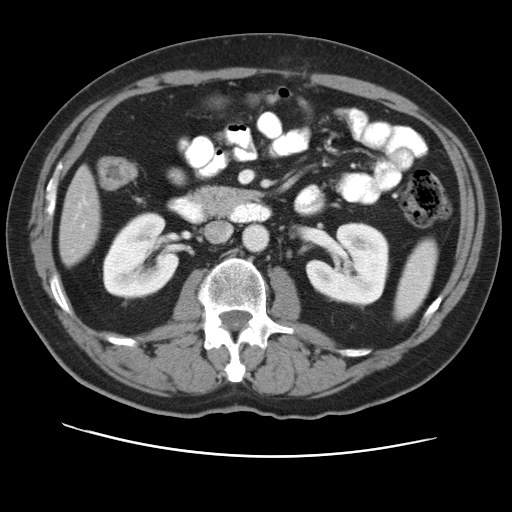
Contrast-enhanced abdominal CT, one axial slice; reconstruction kernel STANDARD; intravenous contrast given; soft-tissue window (W 400 / L 40 HU); 5 mm slice thickness; 512 × 512 image matrix. Male patient, age 59 years. From the clinical record (not read from this slice): diagnosis: colorectal cancer liver metastases, imaged before liver resection; multiple liver metastases: yes; largest metastasis: 6.3 cm; disease in both lobes: yes.
Annotated regions visible in this slice (outlined manually by an expert reader):
- liver: bounding box <60,170,100,263> (left, top, right, bottom; pixels)
- planned liver remnant (the part of the liver to remain after resection): <66,170,100,222>
- portal vein (with intrahepatic branches): <81,201,86,226>